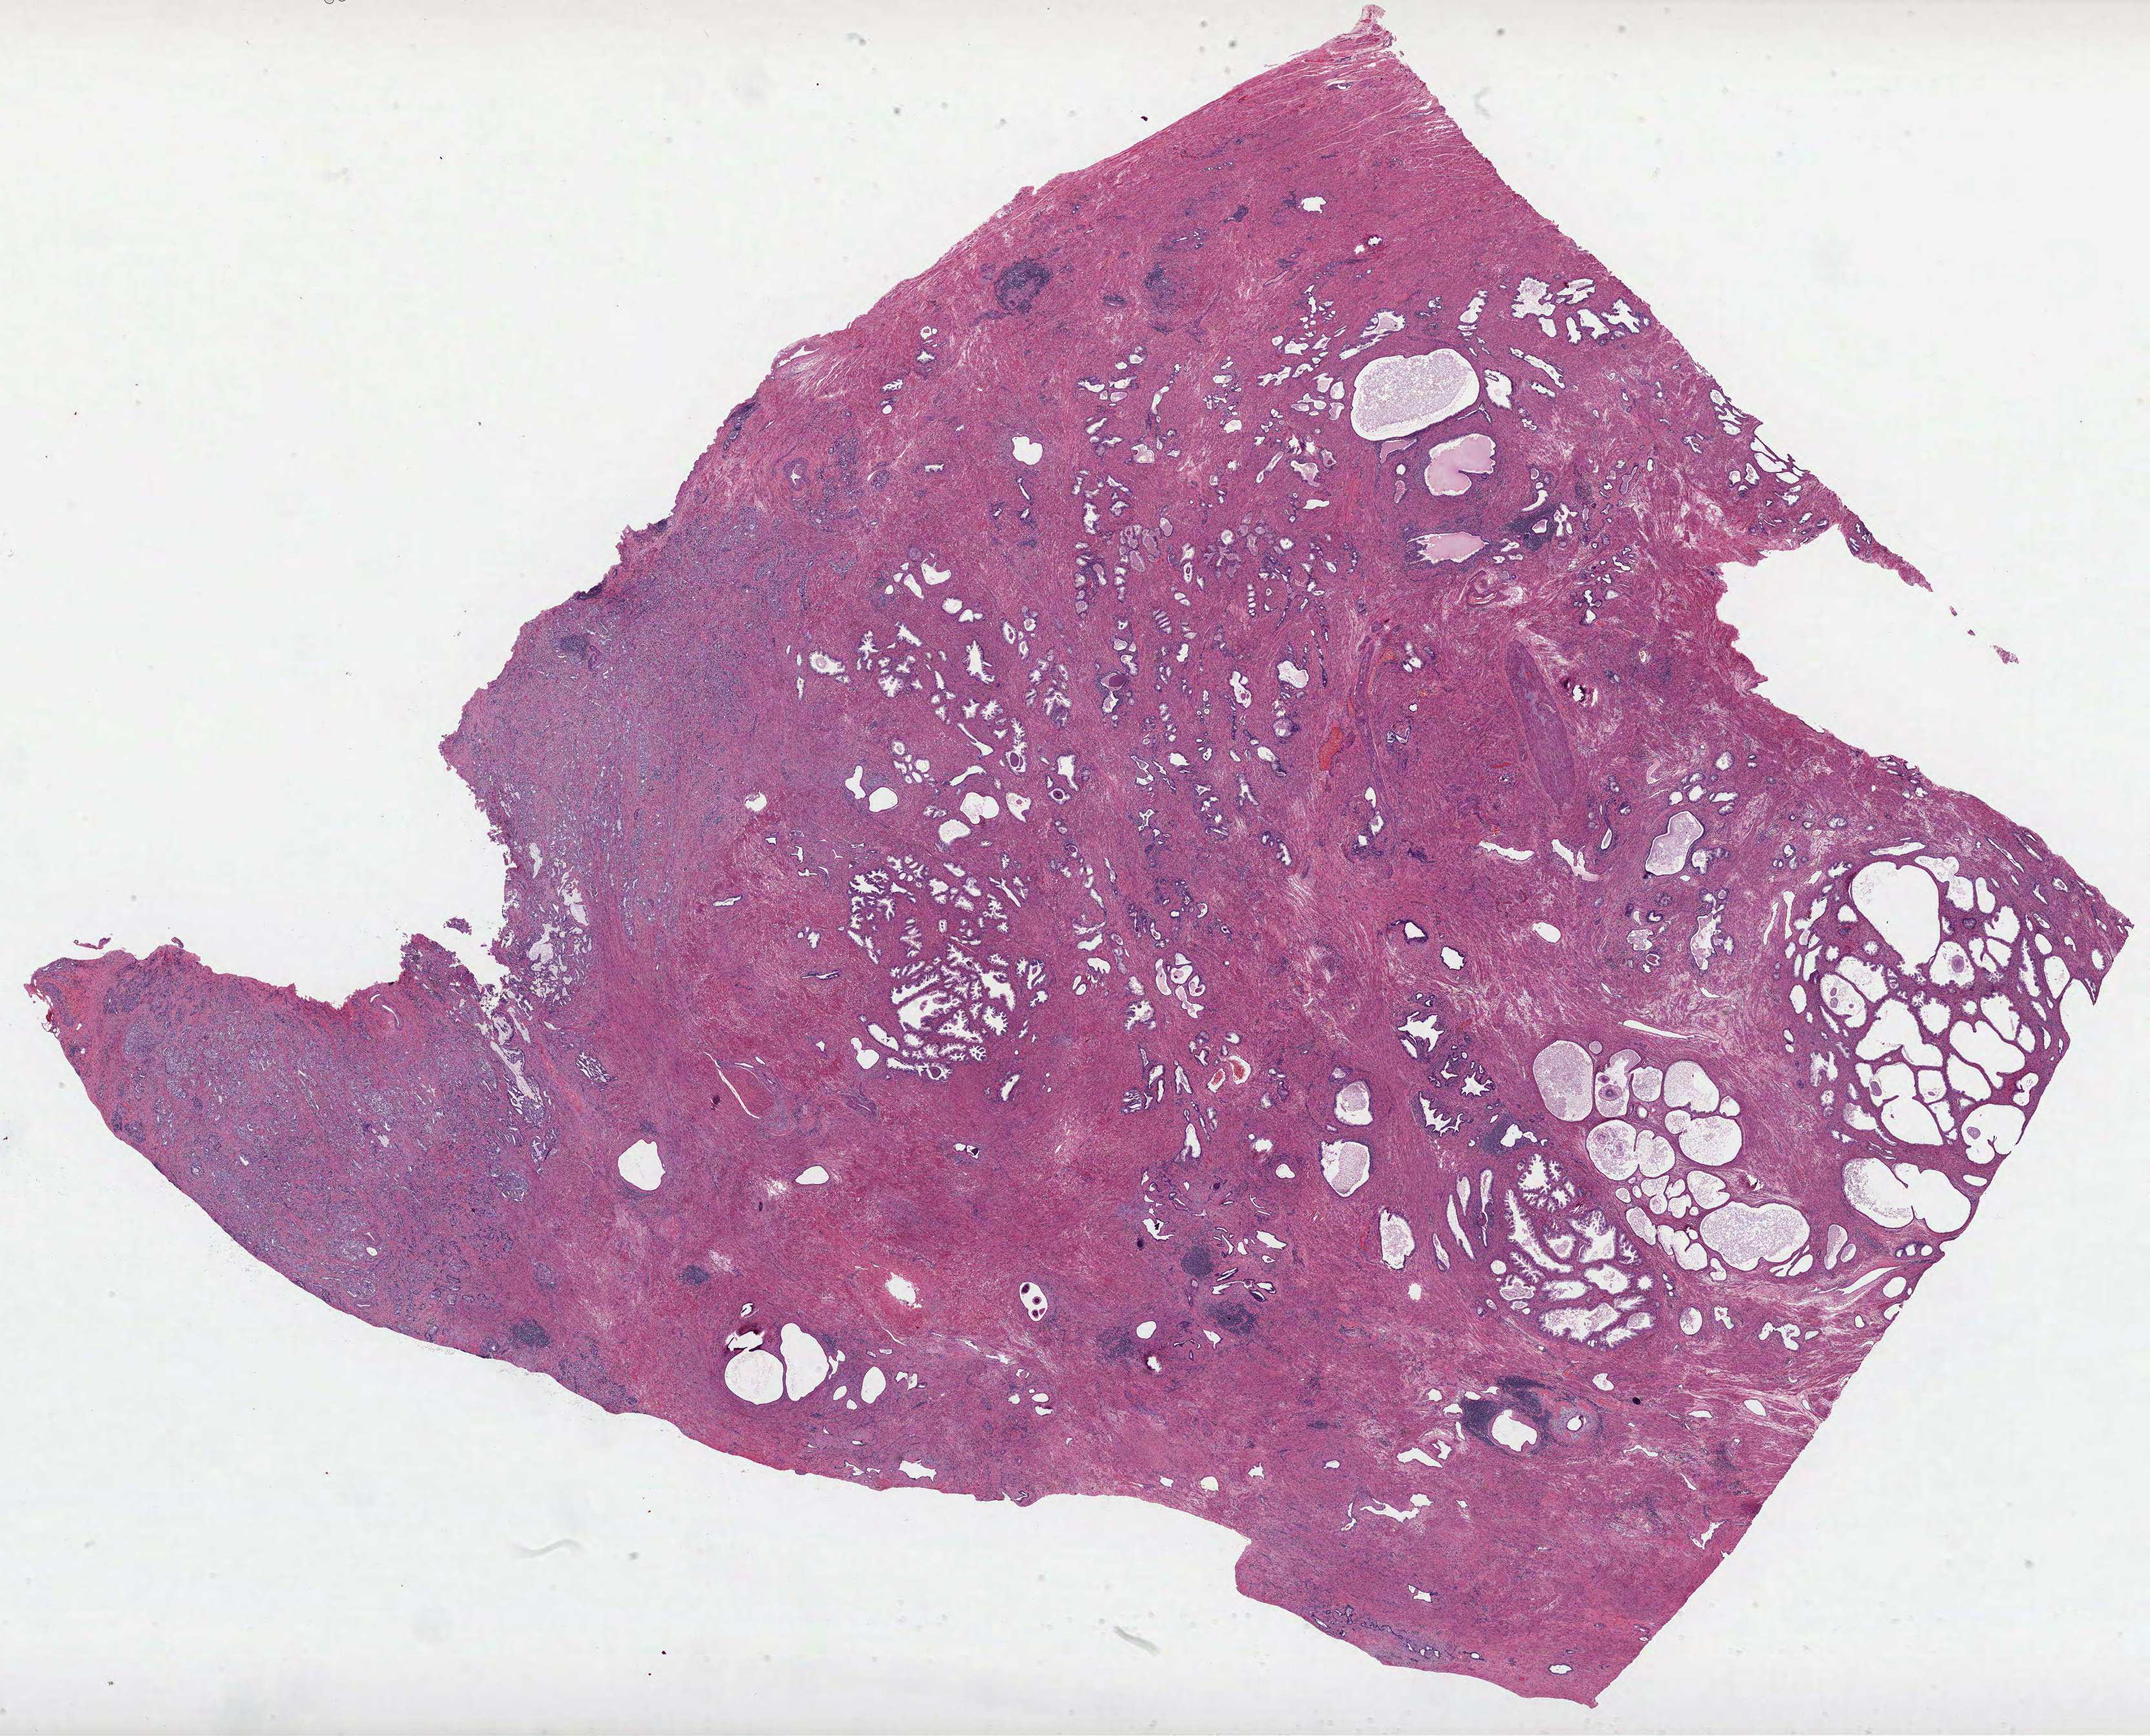
Whole-slide histology image, H&E-stained — whole scanned area (about 26.8 x 21.7 mm) shown as a low-resolution overview. Formalin-fixed paraffin-embedded (FFPE) diagnostic section. Sample: primary tumour, prostate. Male patient; age at initial diagnosis 68 years. Gleason score: 7 (4+3).
• laterality: bilateral
• histologic diagnosis: Acinar cell carcinoma (prostate gland)